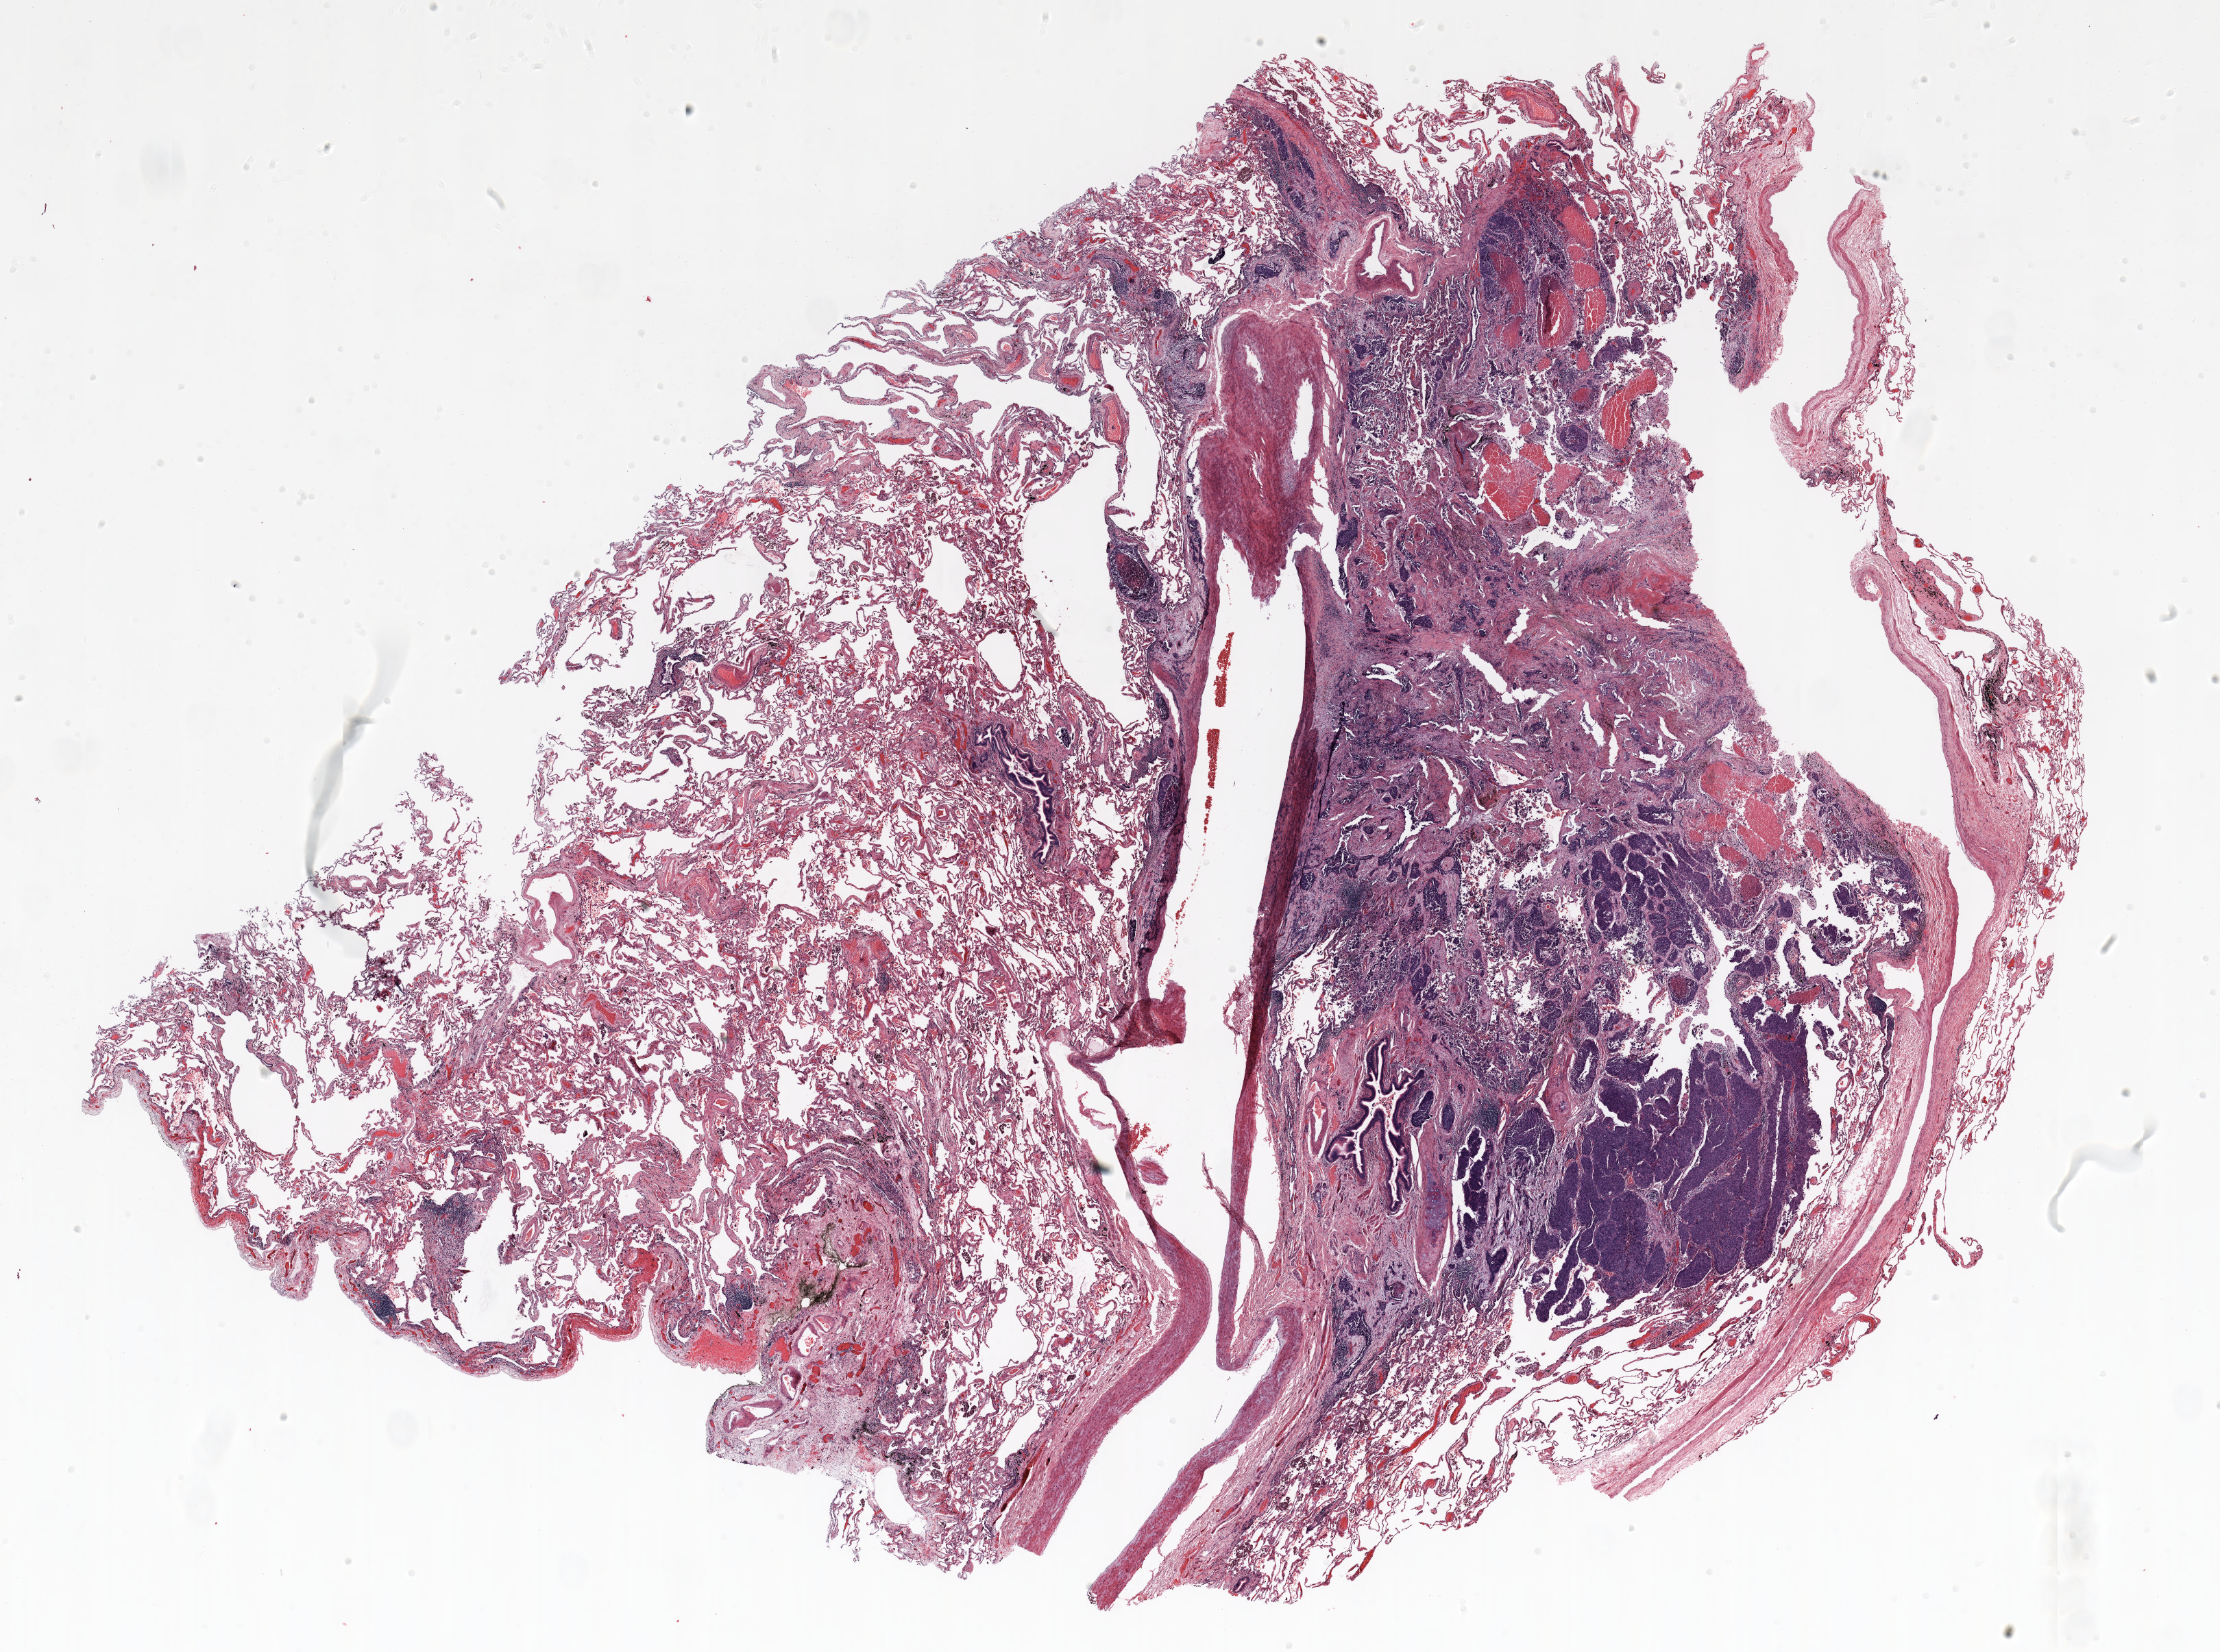
Whole-slide histology image, H&E-stained — shown as a low-resolution overview of the whole scanned area (about 26.0 x 19.4 mm, acquisition: 20x scan); formalin-fixed paraffin-embedded (FFPE) section; lung. Male patient, aged 66 at enrolment. Current smoker at enrolment. Grade: poorly differentiated (G3).
Tumour size (pathology): 15 mm. Participant's lung-cancer diagnosis: Squamous cell carcinoma, NOS. Stage (AJCC 6th edition): IA. Primary tumour location (clinical record): left upper lobe.